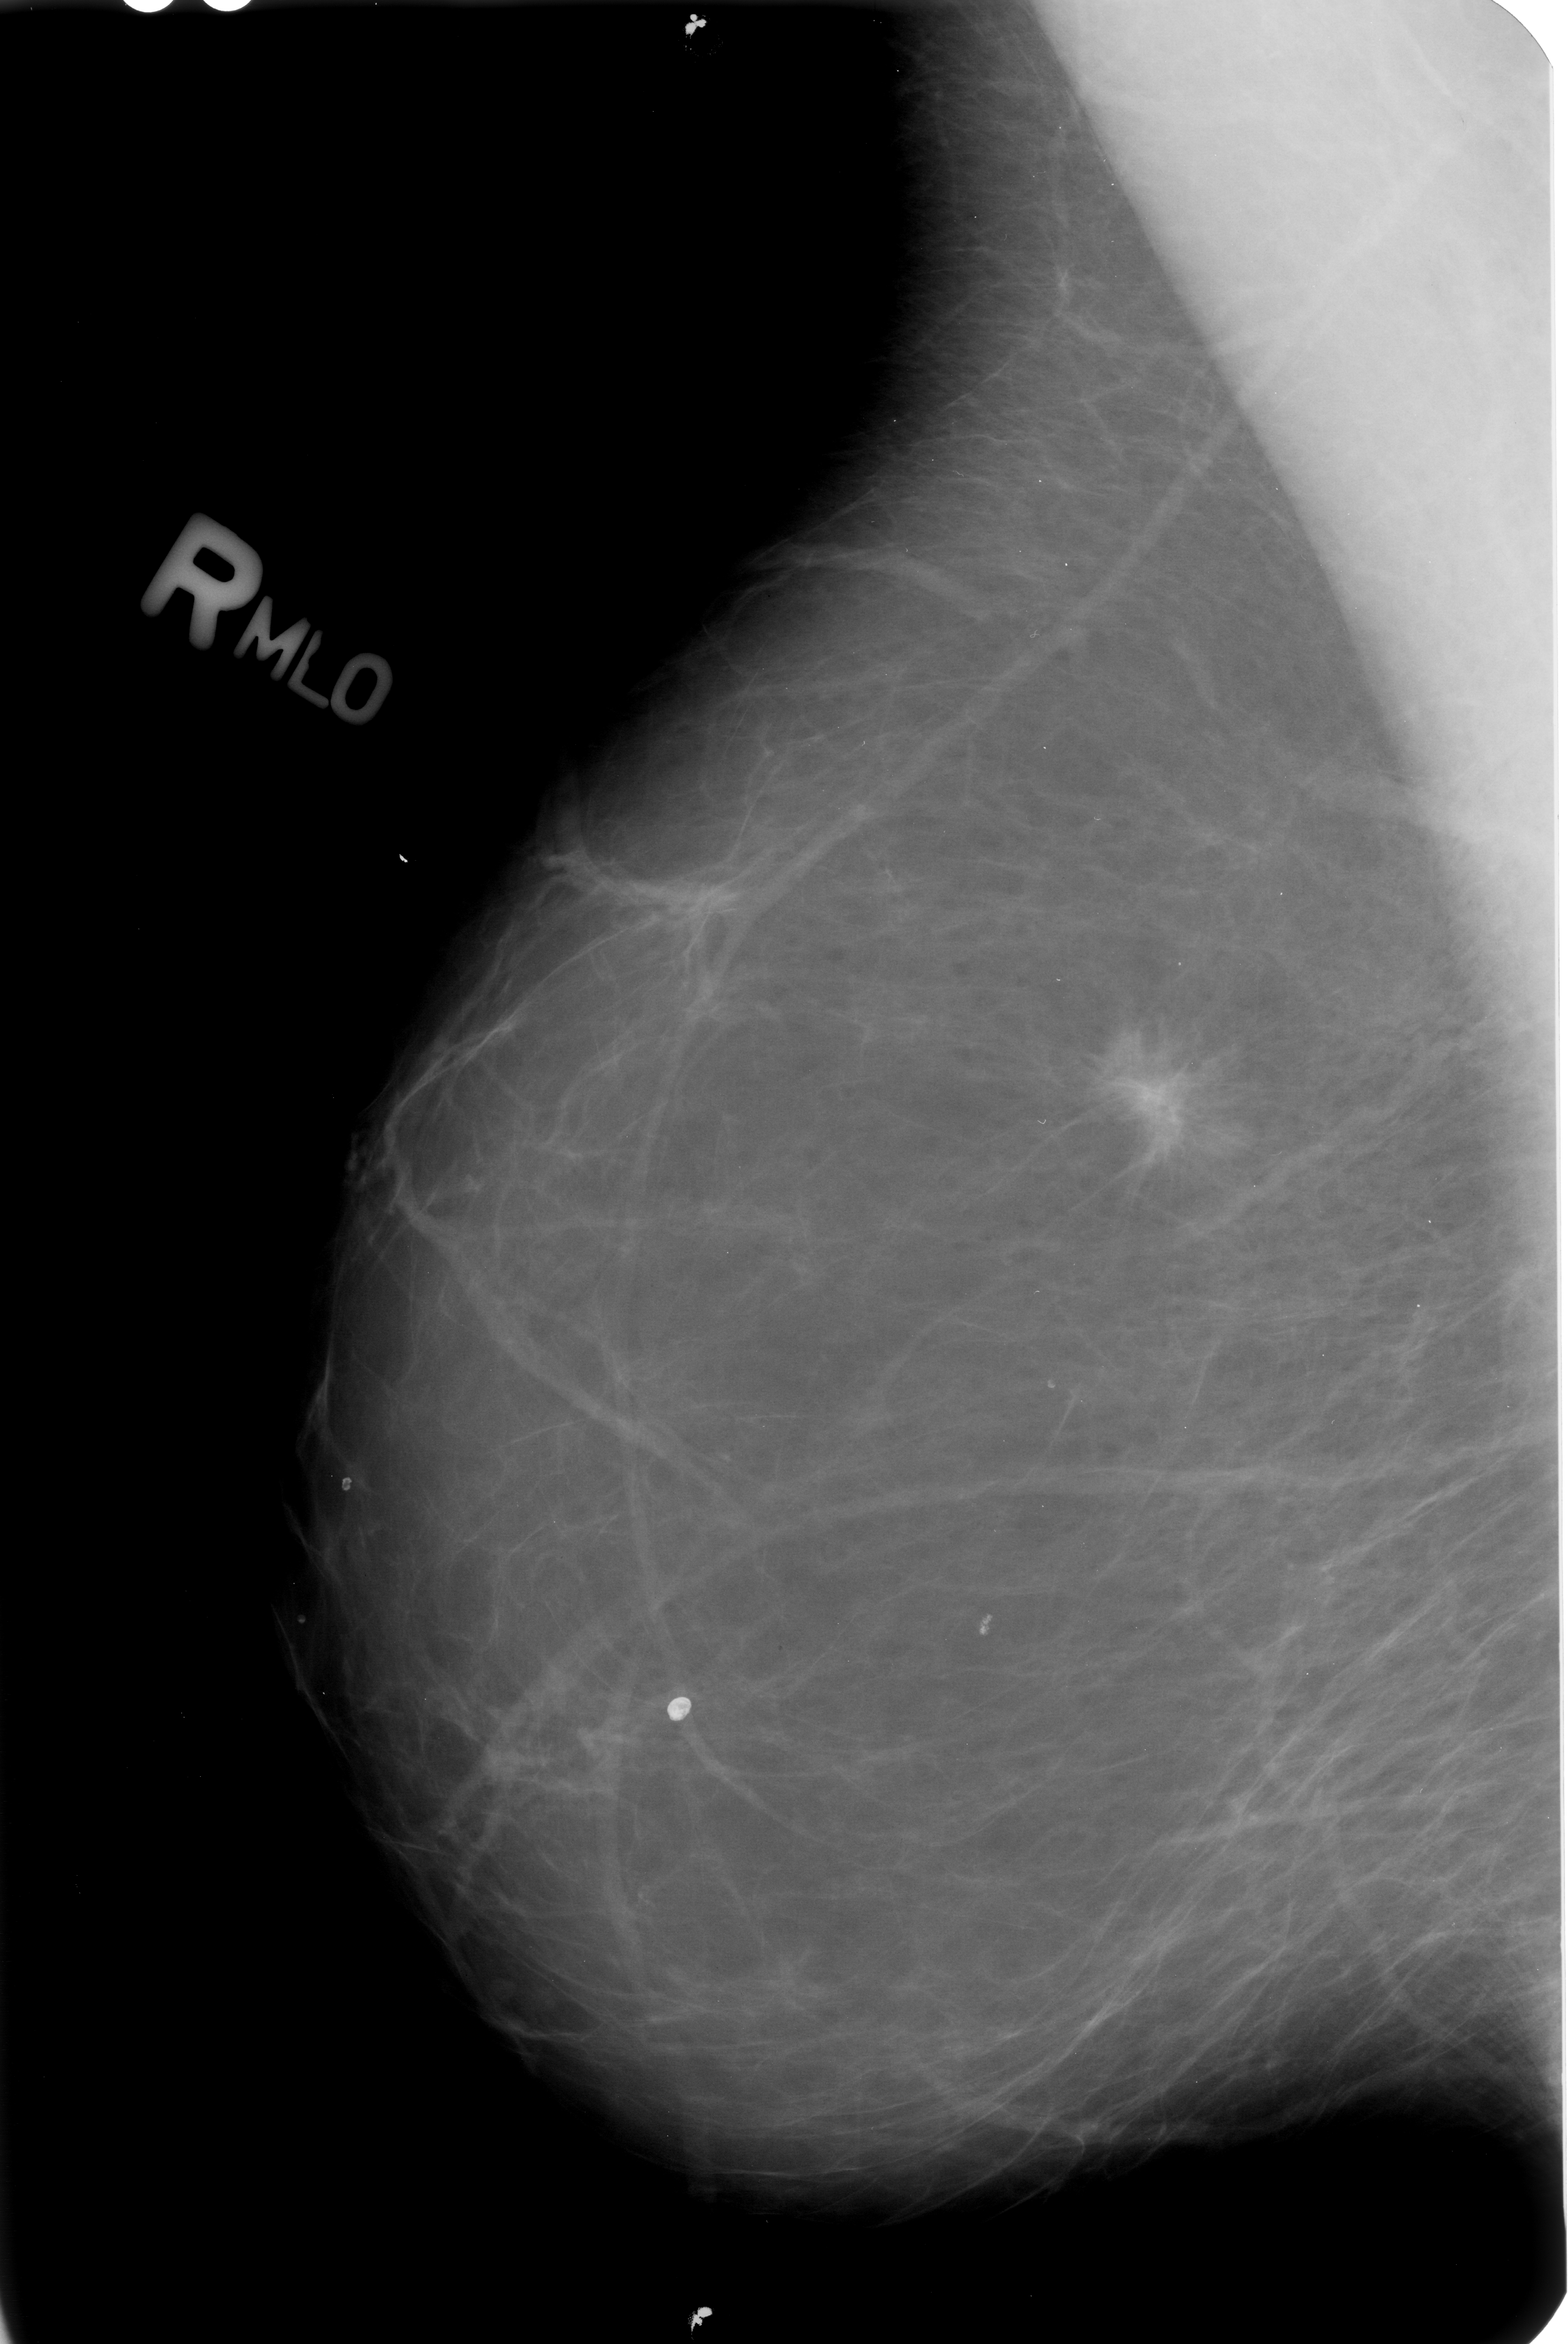
Mammogram (digitized film). Right breast. MLO view. Breast composition: almost entirely fatty (BI-RADS density category 1 of 4). 1568 × 2344 image matrix.
Marked abnormalities (boxes around the expert regions of interest):
- mass, shape irregular / architectural distortion, margins spiculated; BI-RADS assessment category 5; subtlety rating 5 on a 1 (subtle) to 5 (obvious) scale; pathology (as recorded): malignant: bounding box (x1, y1, x2, y2) in pixels: (1085, 1036, 1215, 1176)